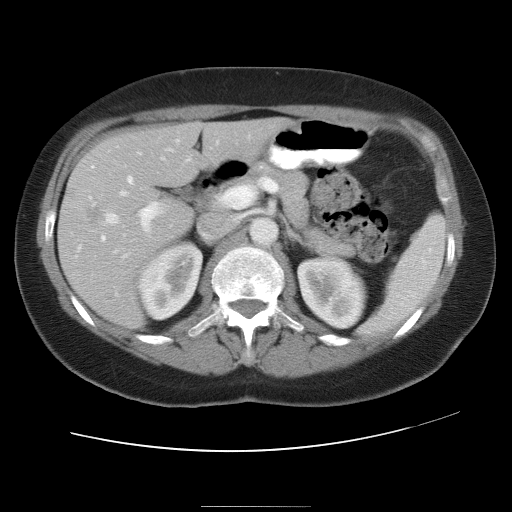
Contrast-enhanced abdominal CT, one axial slice. Position 18 of 30 along the scan axis. Reconstruction kernel STANDARD. 120 kVp. Soft-tissue window (W 400 / L 40 HU). 7.5 mm slice thickness. 512 × 512 image matrix, field of view 376 × 376 mm. Female patient, age 52 years. Case-level facts recorded for this patient, not image findings: diagnosis: colorectal cancer liver metastases, imaged before liver resection; multiple liver metastases: no; largest metastasis: 3 cm; disease in both lobes: yes.
Outlined on this slice (outlined manually by an expert reader):
- hepatic veins: bounding box <106,157,164,223> (left, top, right, bottom; pixels)
- liver: <59,118,286,327>
- planned liver remnant (the part of the liver to remain after resection): <153,118,286,179>
- portal vein (with intrahepatic branches): <101,141,179,241>
- liver metastasis: <95,210,100,218>